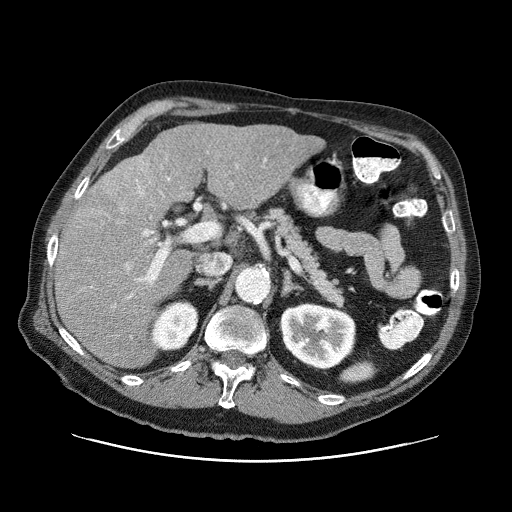
Contrast-enhanced abdominal CT (liver protocol), one axial slice. 120 kVp. One of 3 acquisitions stored at this slice position. Soft-tissue window (W 400 / L 40 HU). 2.5 mm slice thickness. 512 × 512 image matrix, field of view 400 × 400 mm. From the clinical record (not read from this slice): diagnosis: hepatocellular carcinoma (patient treated with transarterial chemoembolisation; whether this scan precedes or follows treatment is not stated here); TNM stage (as recorded): Stage-IIIA; Child-Pugh class: A; tumour nodularity: multinodular; tumour size: 6 cm.
Structures marked on this image (semi-automatically segmented with operator editing):
- liver parenchyma outside the tumour (the mass and vessels are separate outlines, so this box may not span the whole liver): box from (x=55, y=124) to (x=324, y=366) px
- mass: (x=95, y=157)–(x=152, y=218)
- liver vessels: (x=91, y=159)–(x=266, y=299)